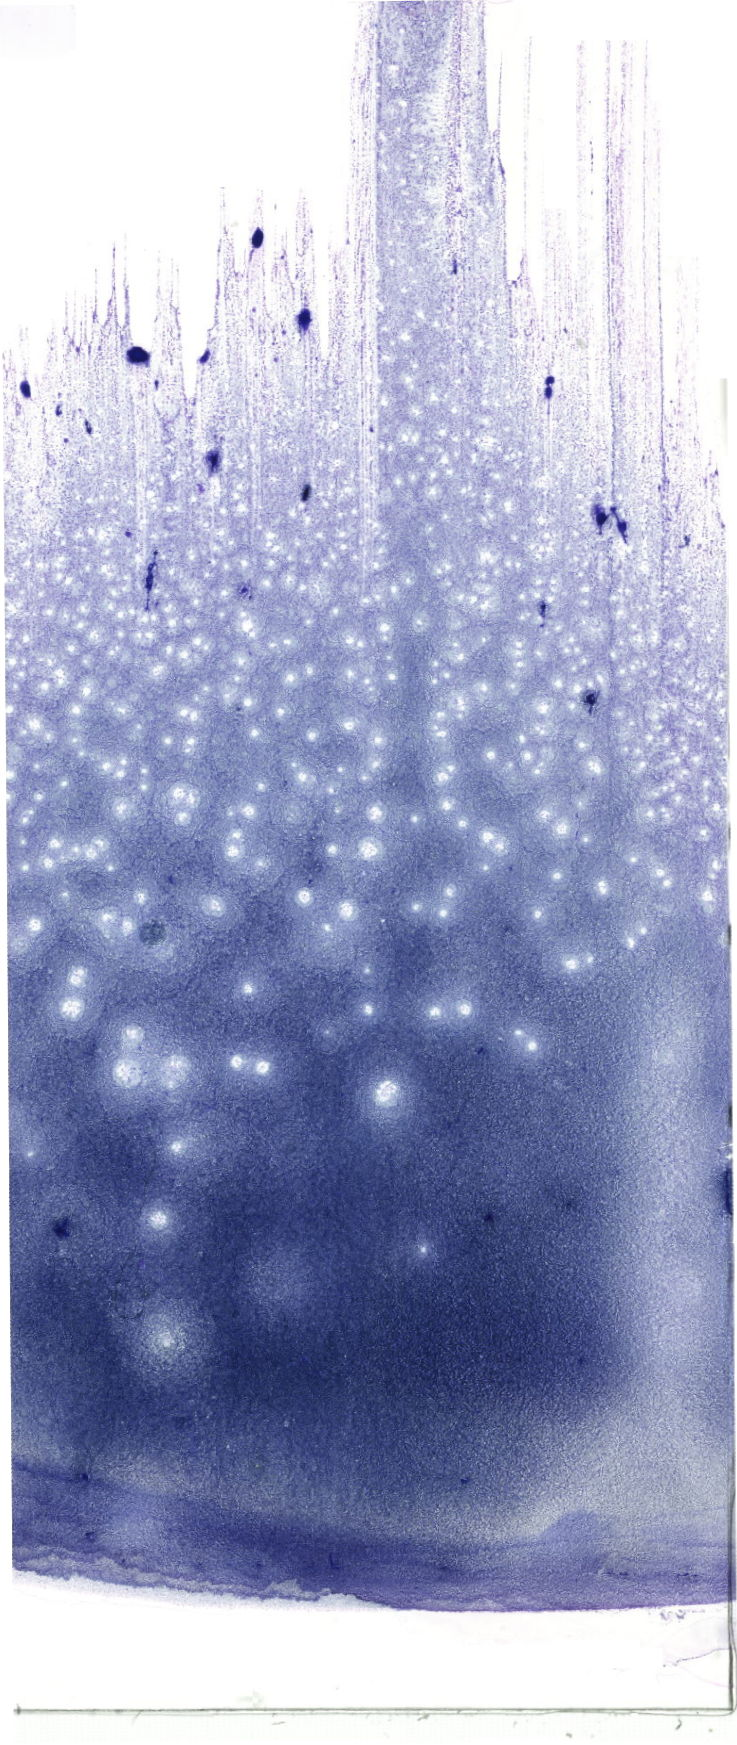
May-Grünwald–Giemsa-stained marrow aspirate smear (whole slide) — shown as a low-resolution overview of the whole scanned area (about 20.9 x 49.5 mm). Male patient.
- diagnosis: B Acute Lymphoblastic Leukemia